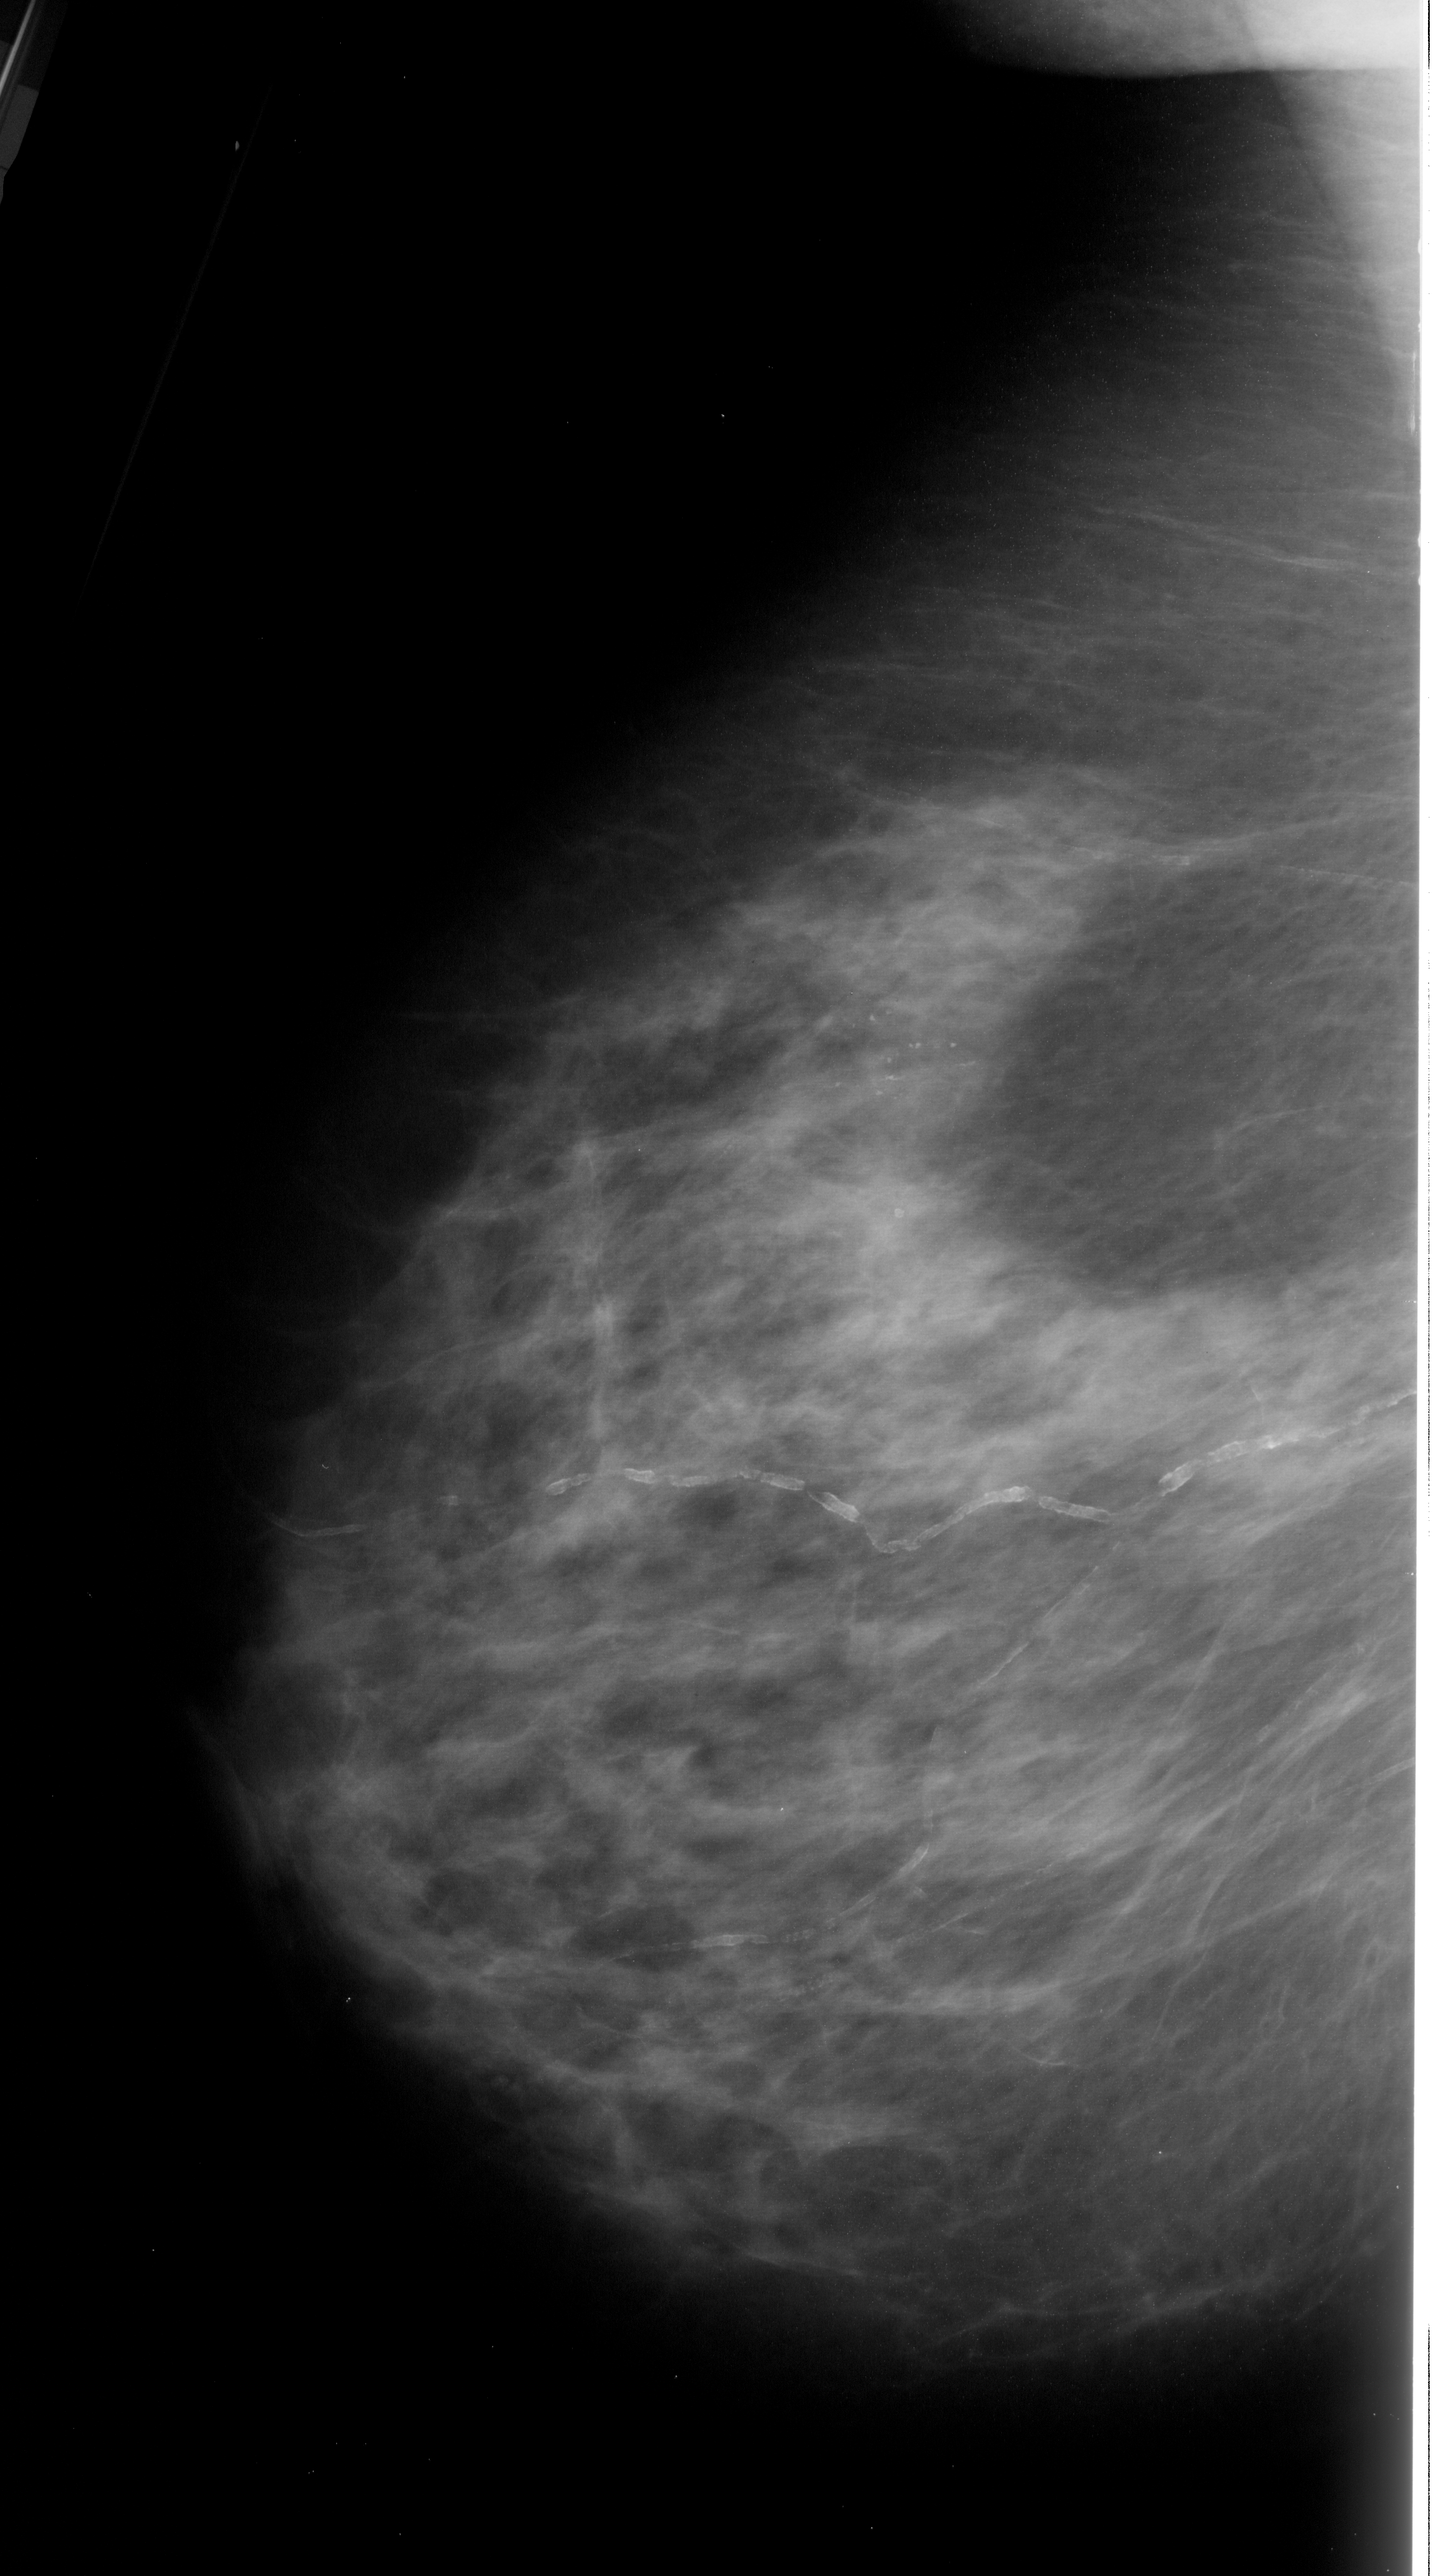
Mammogram (digitized film), left breast, mediolateral oblique (MLO) view, BI-RADS breast density category 3 (scale 1–4).
Marked abnormality: calcifications, morphology pleomorphic, distribution linear; BI-RADS assessment category 4; subtlety rating 3 on a 1 (subtle) to 5 (obvious) scale; pathology (as recorded): malignant.